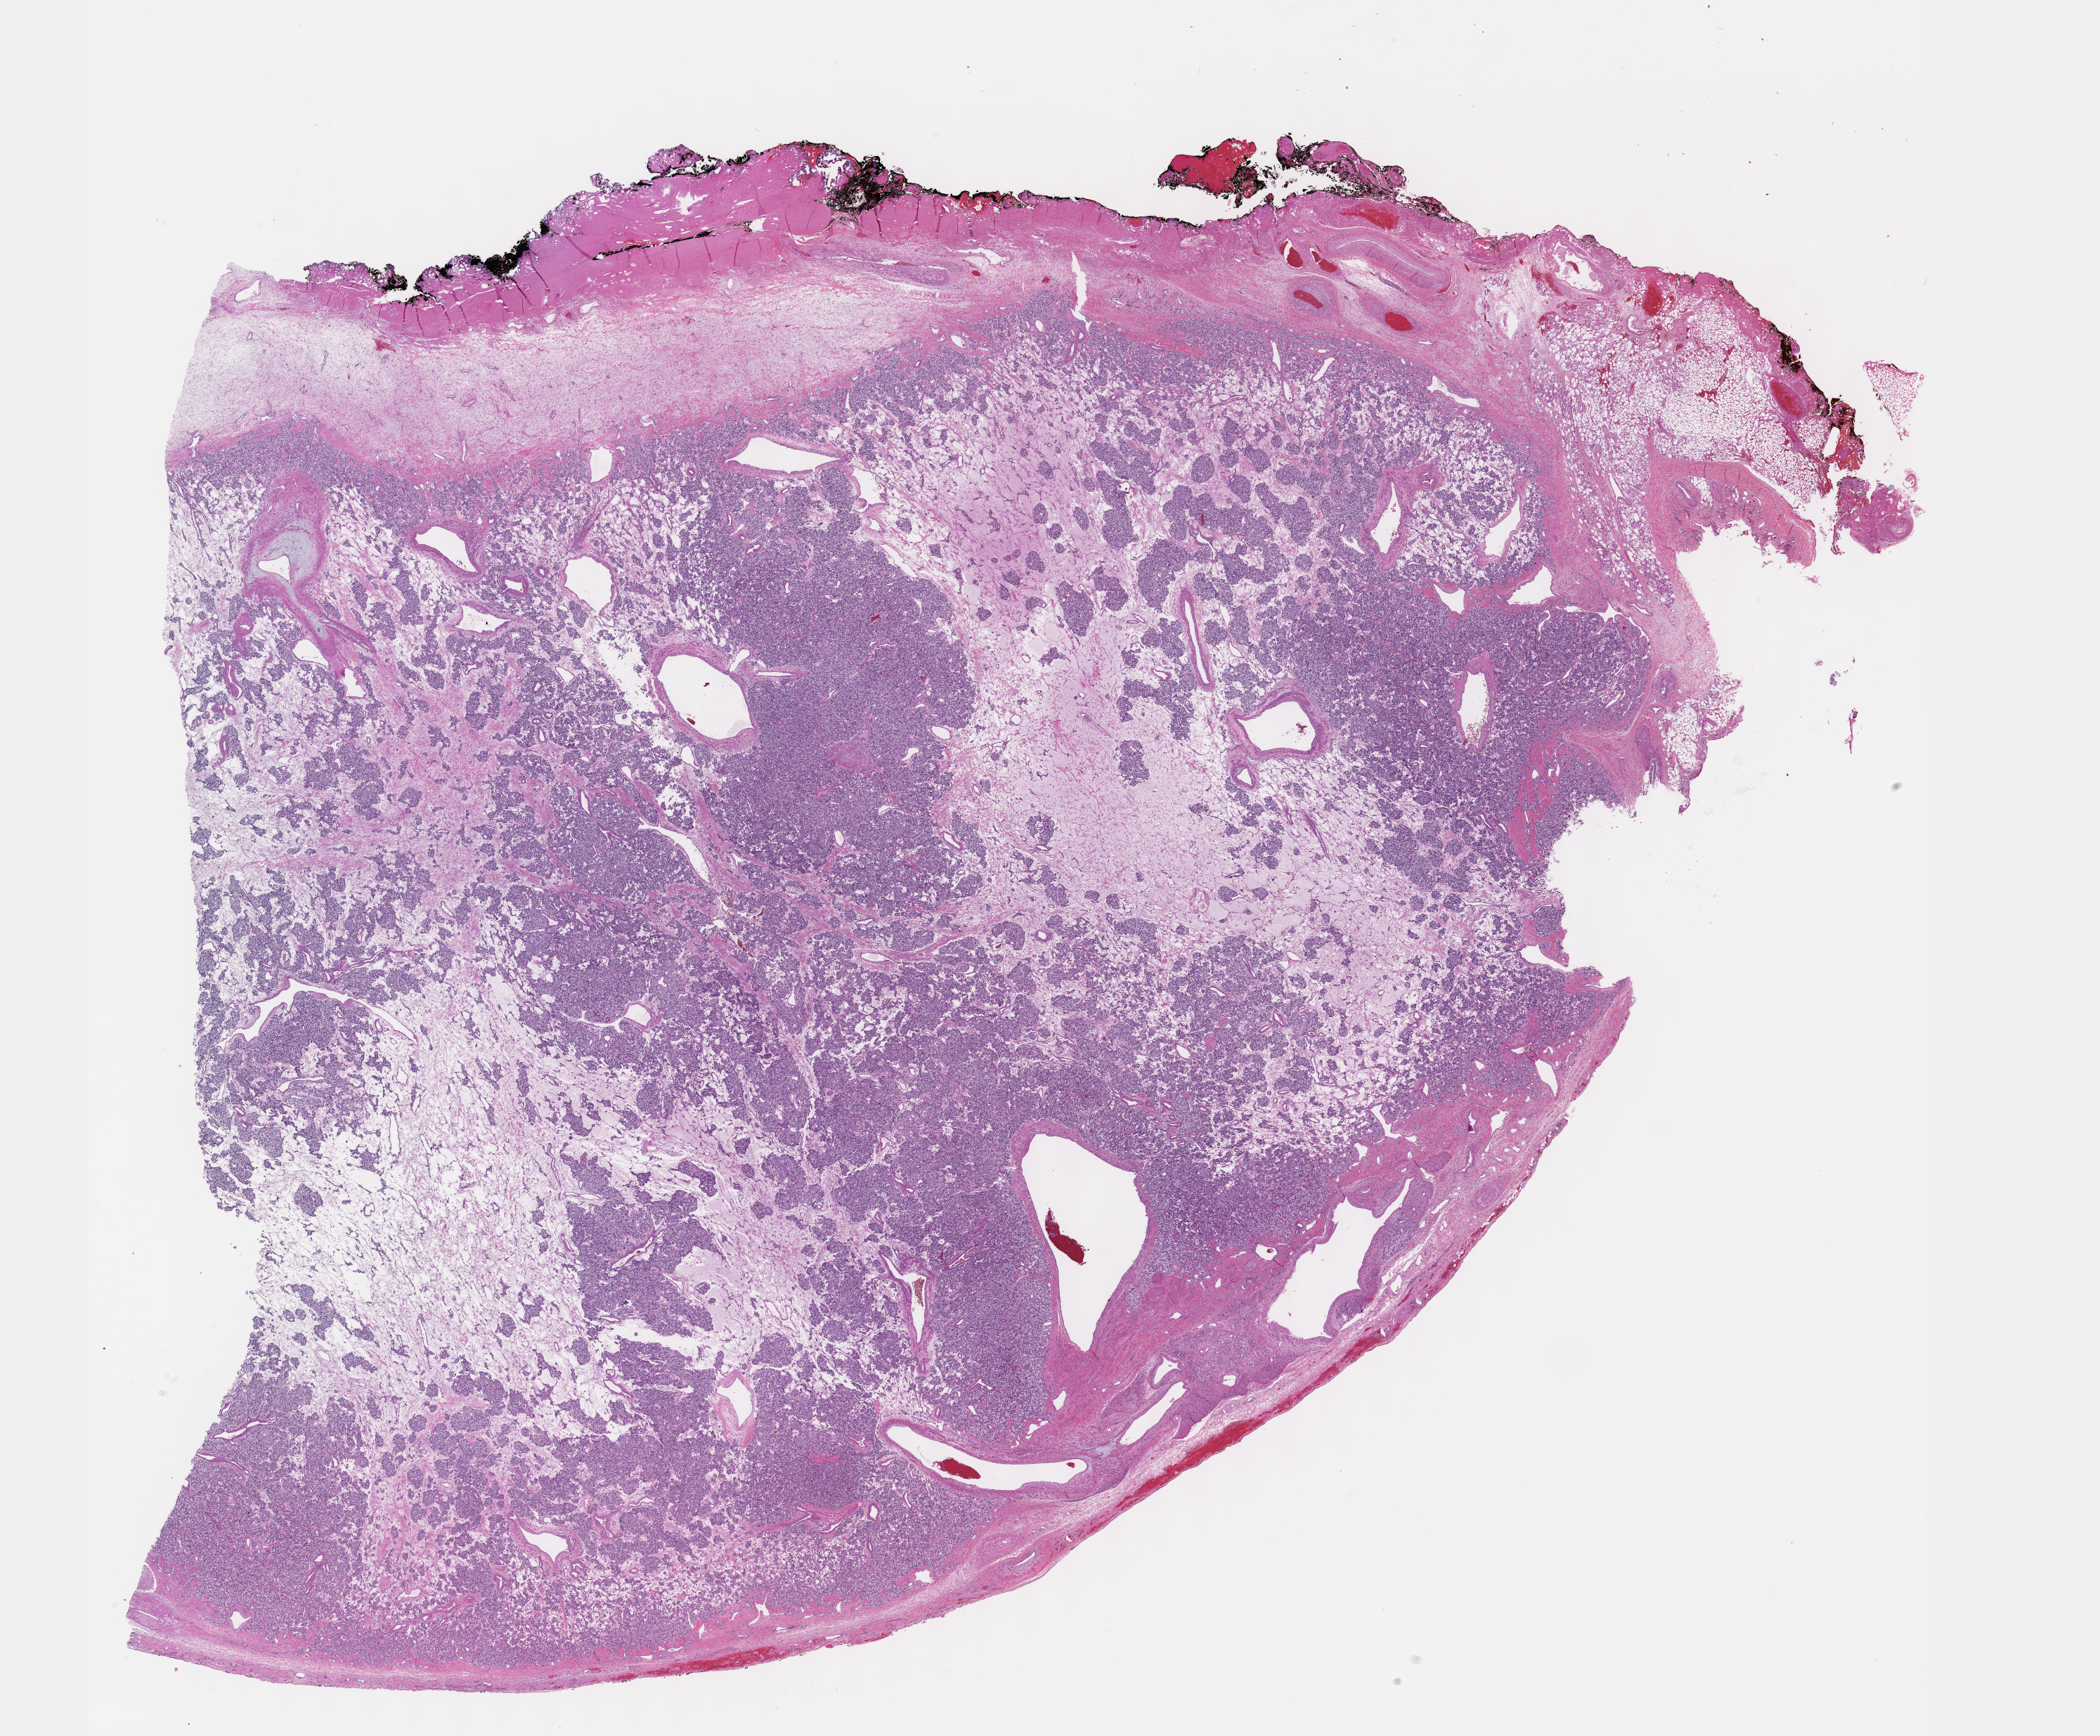
Whole-slide histology image, Hematoxylin and eosin (H&E) stained, low-resolution overview of the scanned area, about 24.1 x 20.0 mm (acquisition: 40x scan), formalin-fixed paraffin-embedded (FFPE) diagnostic section, sample: primary tumour, connective, subcutaneous and other soft tissues. Female, age 50 years at initial diagnosis.
Diagnosis: Extra-adrenal paraganglioma, NOS.